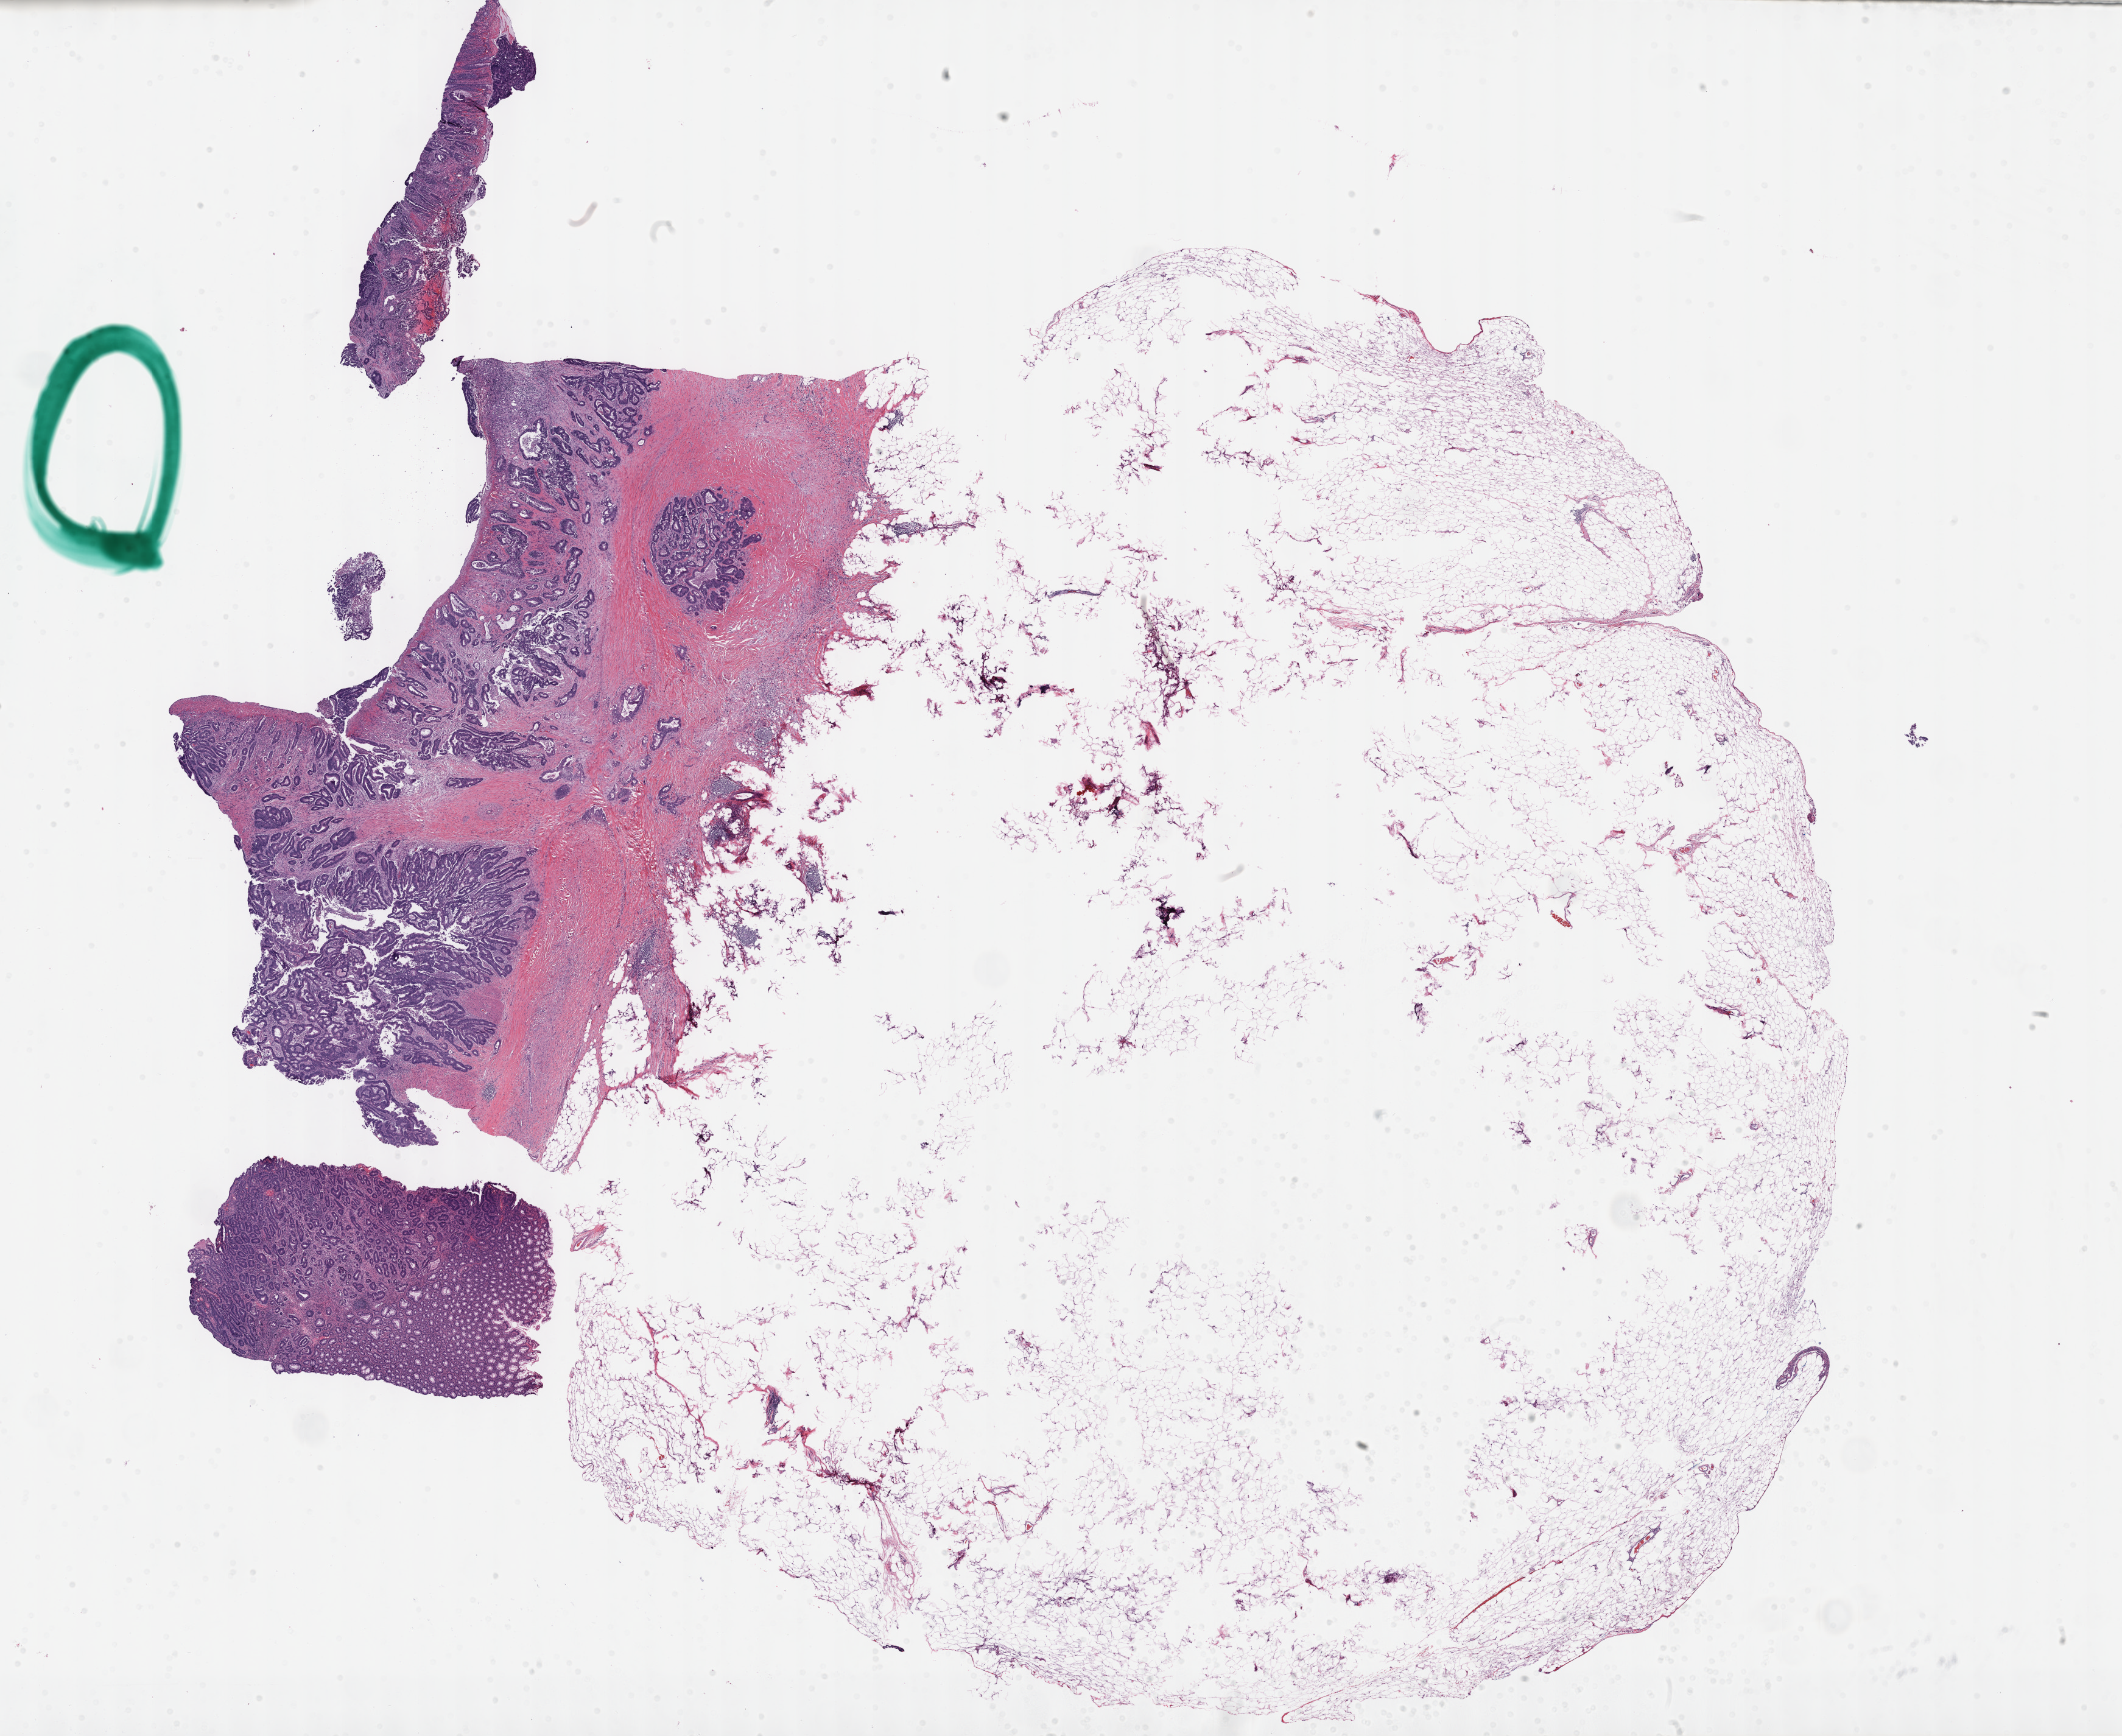
H&E-stained whole-slide image — shown as a low-resolution overview of the whole scanned area (about 28.2 x 23.1 mm, acquisition: 40x scan), FFPE section, primary tumour sample from the colon. Patient: male, age at initial diagnosis 71 years.
AJCC pathologic stage: IIIB (7th edition). Histologic diagnosis: Adenocarcinoma, NOS.